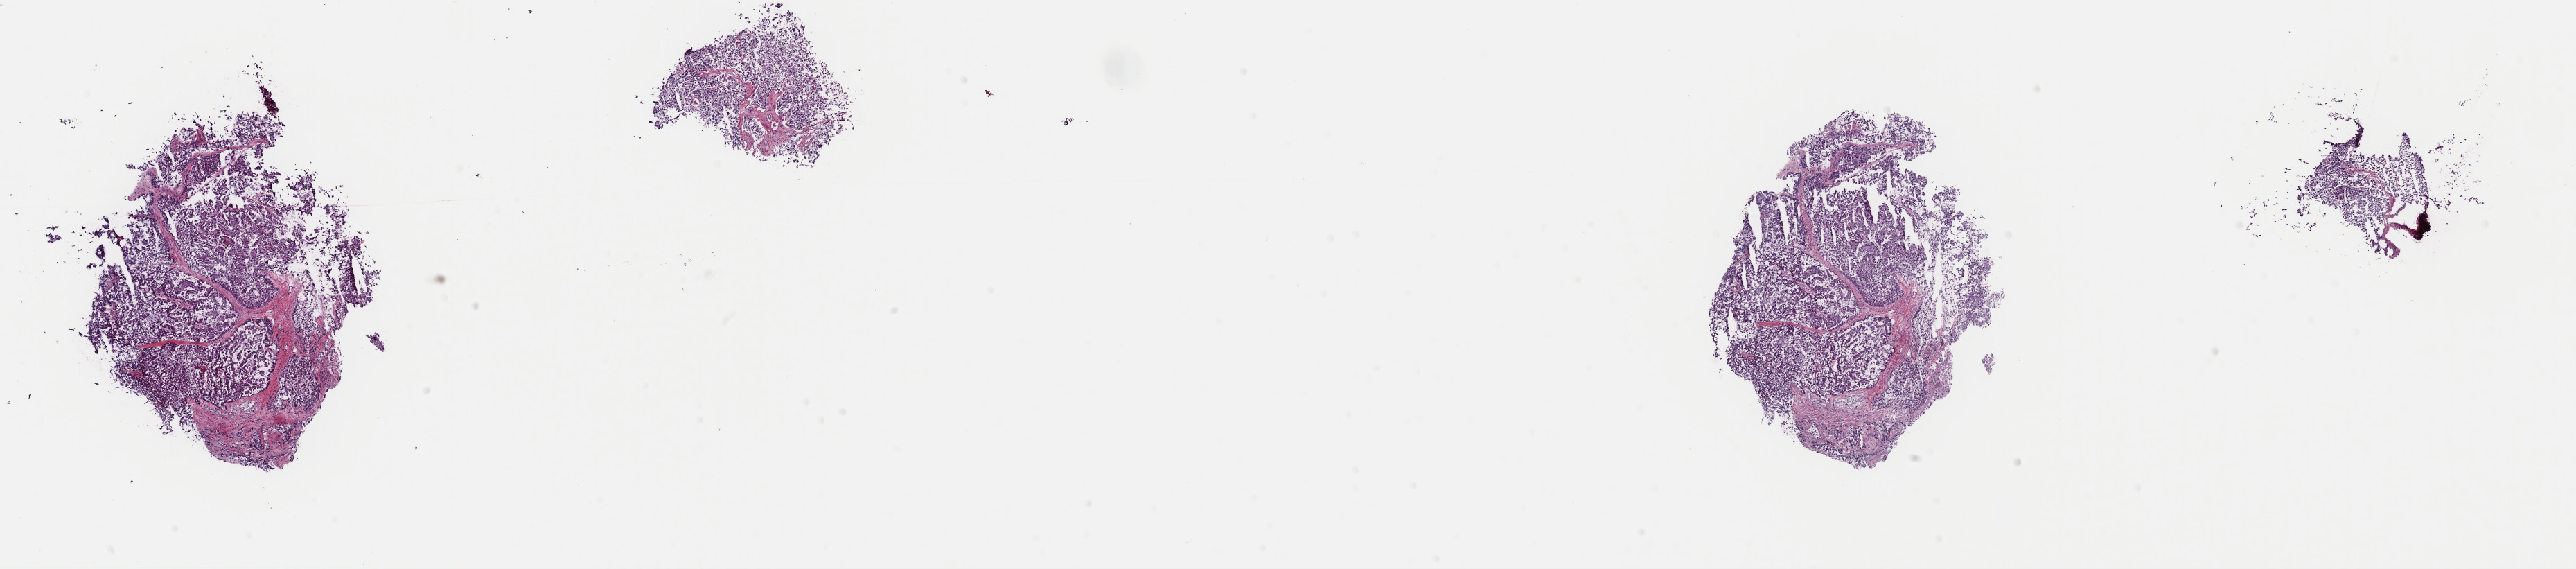
Whole-slide histology image, H&E-stained, a low-resolution overview of the entire scanned area, about 29.4 x 6.5 mm (acquisition: 40x scan). Frozen section from the top of the tissue portion. Kidney, primary tumour sample. Male patient; age at initial diagnosis 70 years. Slide review estimates, as recorded: tumour cells 90%, tumour nuclei 100%, normal cells 0%, stromal cells 10%, necrosis 0%. Inflammatory infiltration, as recorded: lymphocyte infiltration 0%, monocyte infiltration 2%, neutrophil infiltration 0%.
Pathologic diagnosis: Papillary adenocarcinoma, NOS. AJCC pathologic stage: III. Laterality: left.